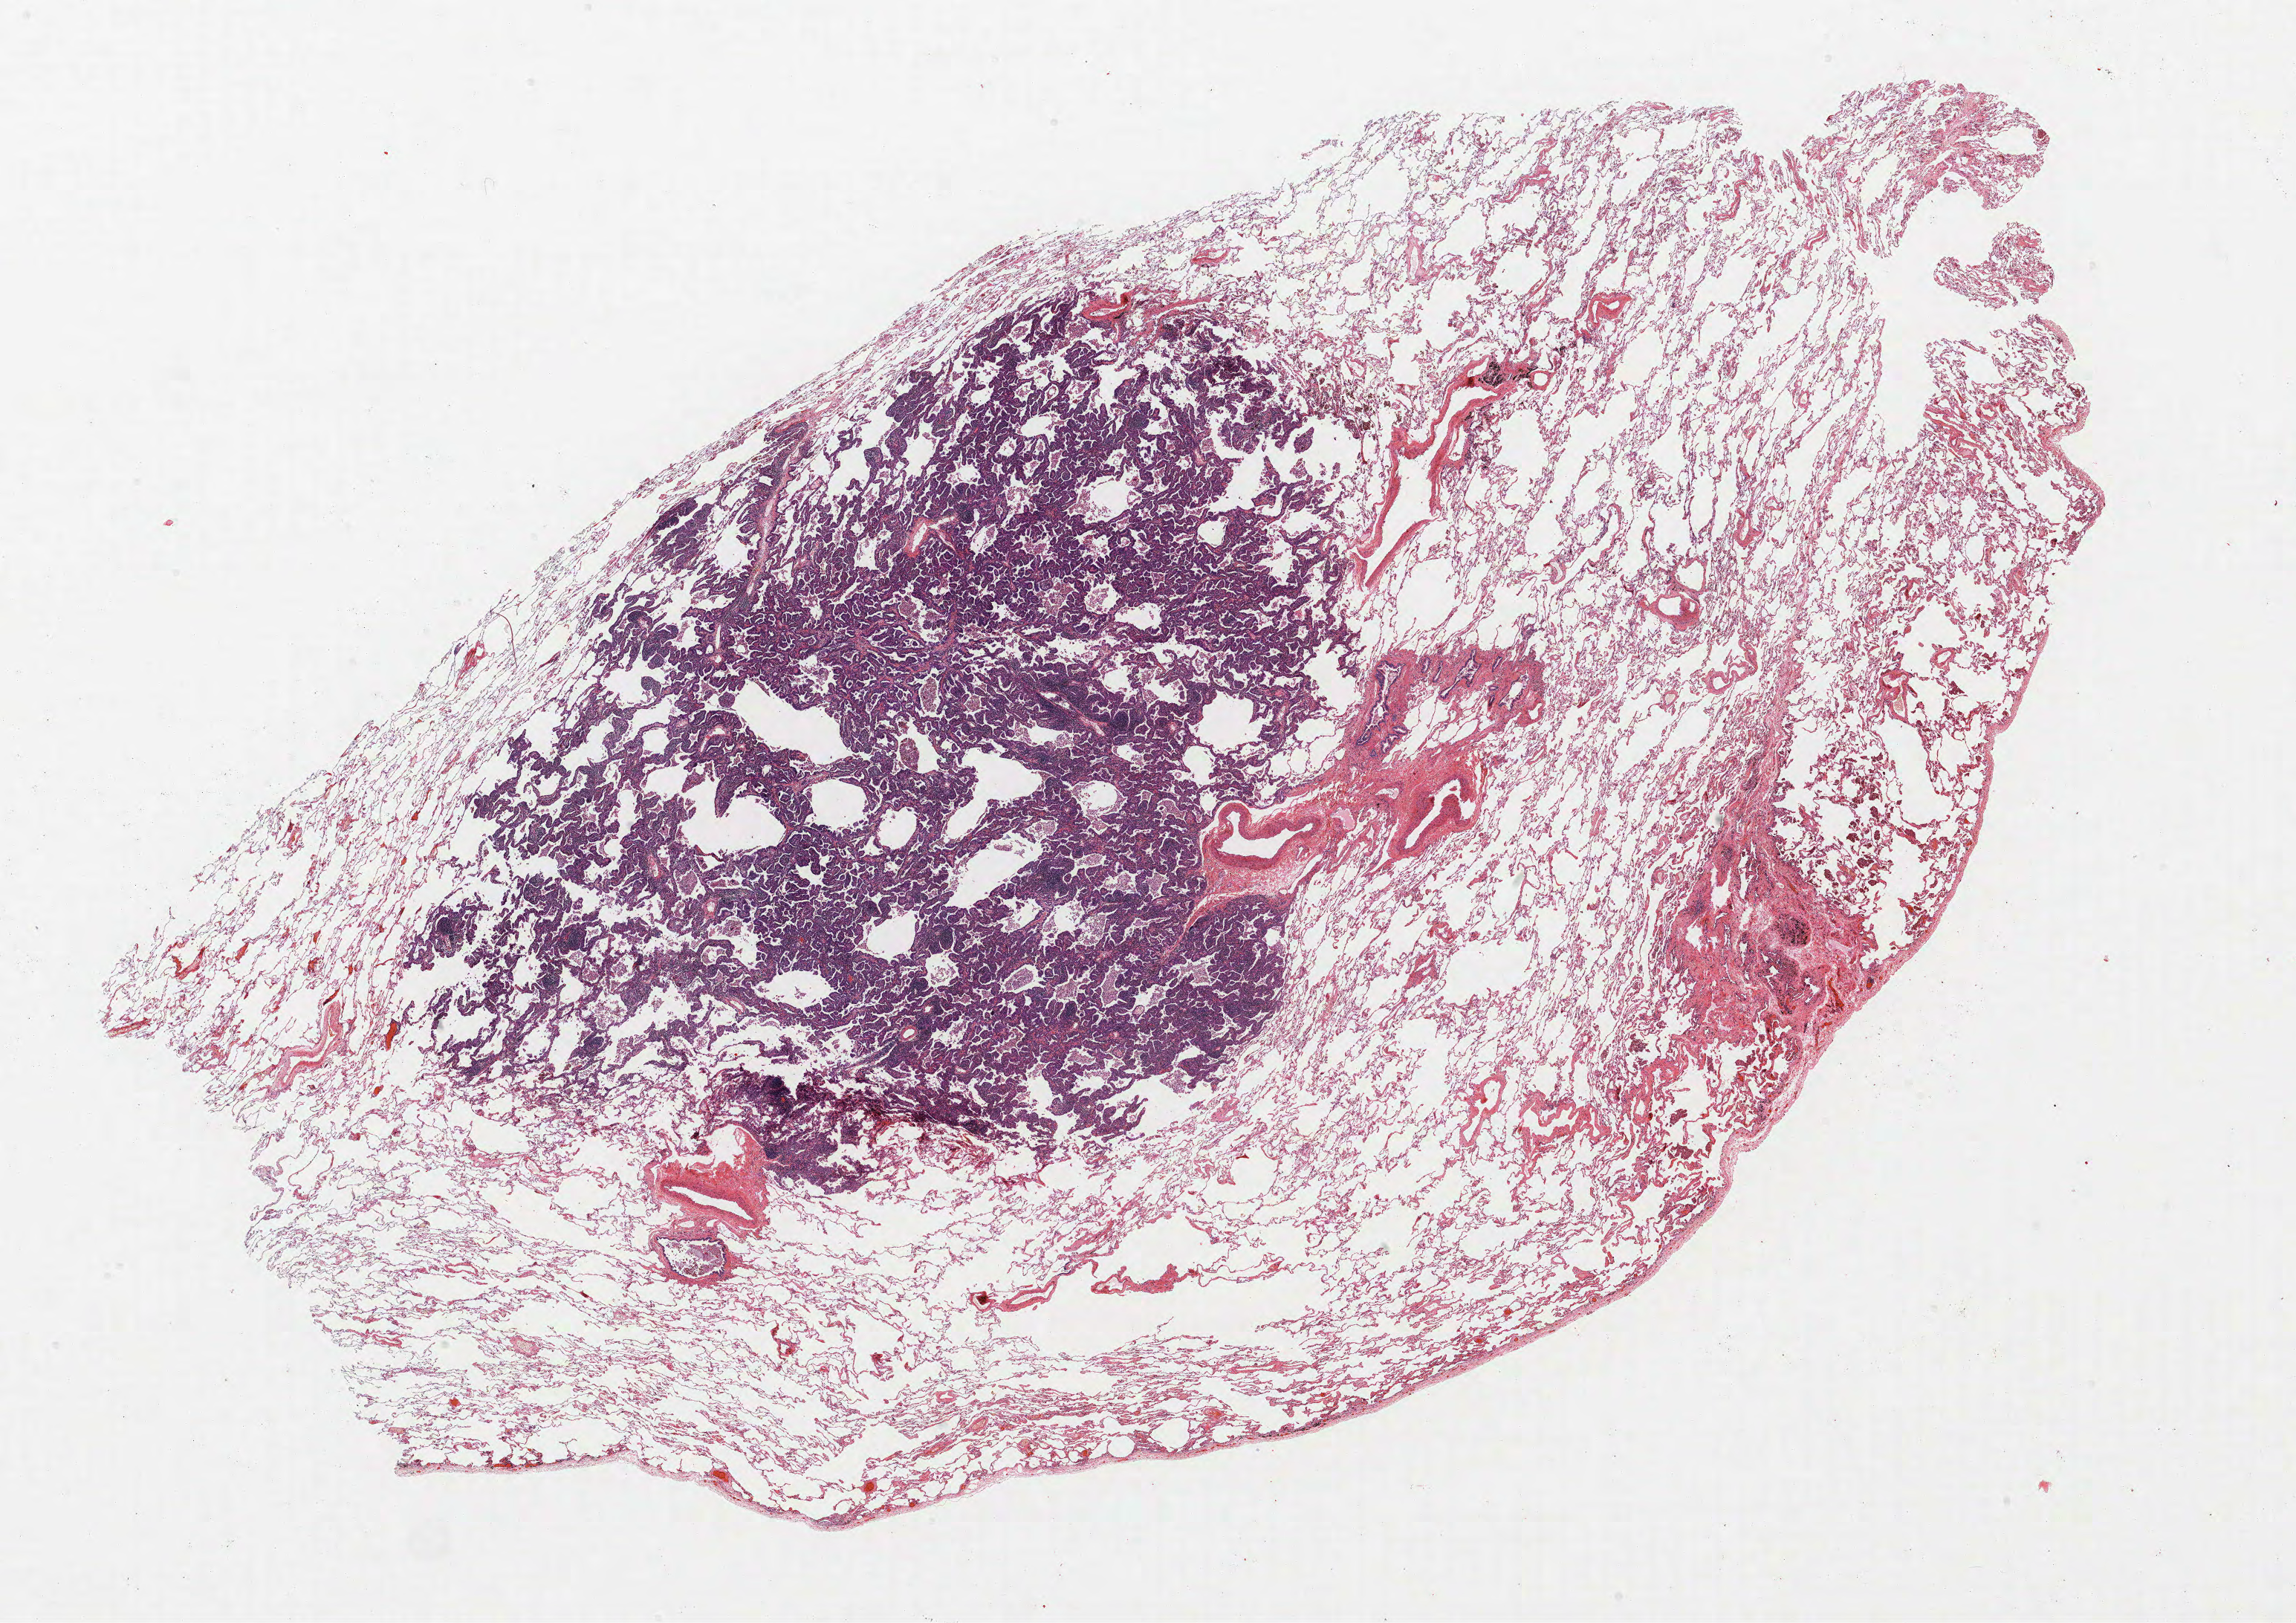
Whole-slide histology image, H&E — whole scanned area (about 24.7 x 17.5 mm, slide scanned at 40x) shown as a low-resolution overview; formalin-fixed paraffin-embedded (FFPE) section; lung tissue. Male, age 58 at enrolment. Grade: moderately differentiated (G2).
Primary tumour location (clinical record): right upper lobe. Participant's lung-cancer diagnosis: Bronchiolo-alveolar adenocarcinoma, NOS. Tumour size (pathology): 6 mm. Stage (AJCC 6th edition): IA. Note: participant had 2 primary lung cancers recorded; fields above describe the first.